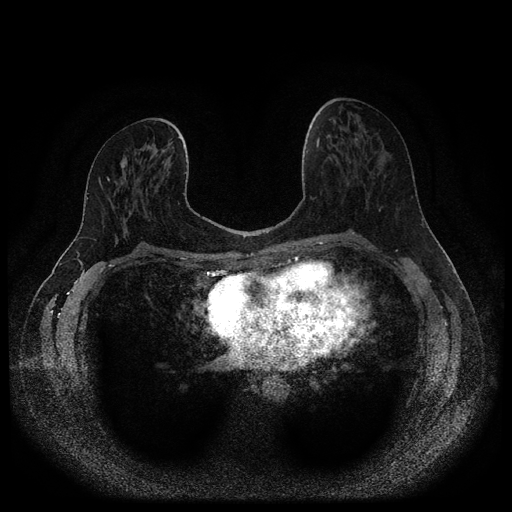
Breast MRI (dynamic contrast-enhanced, multi-phase), one axial slice. Position 50 of 116 along the scan axis. Dynamic contrast-enhanced series, time point 2 of 5 at this slice position (early post-contrast). 1.5 T. TE 2.7 ms, TR 5.4 ms. 512 × 512 image matrix, field of view 330 × 330 mm. Patient: female, 46 years.
Structures marked on this image (semi-automatically segmented with operator editing):
- breast lesion (labelled benign in the annotation): bounding box [x1, y1, x2, y2] px = [120, 158, 127, 169]